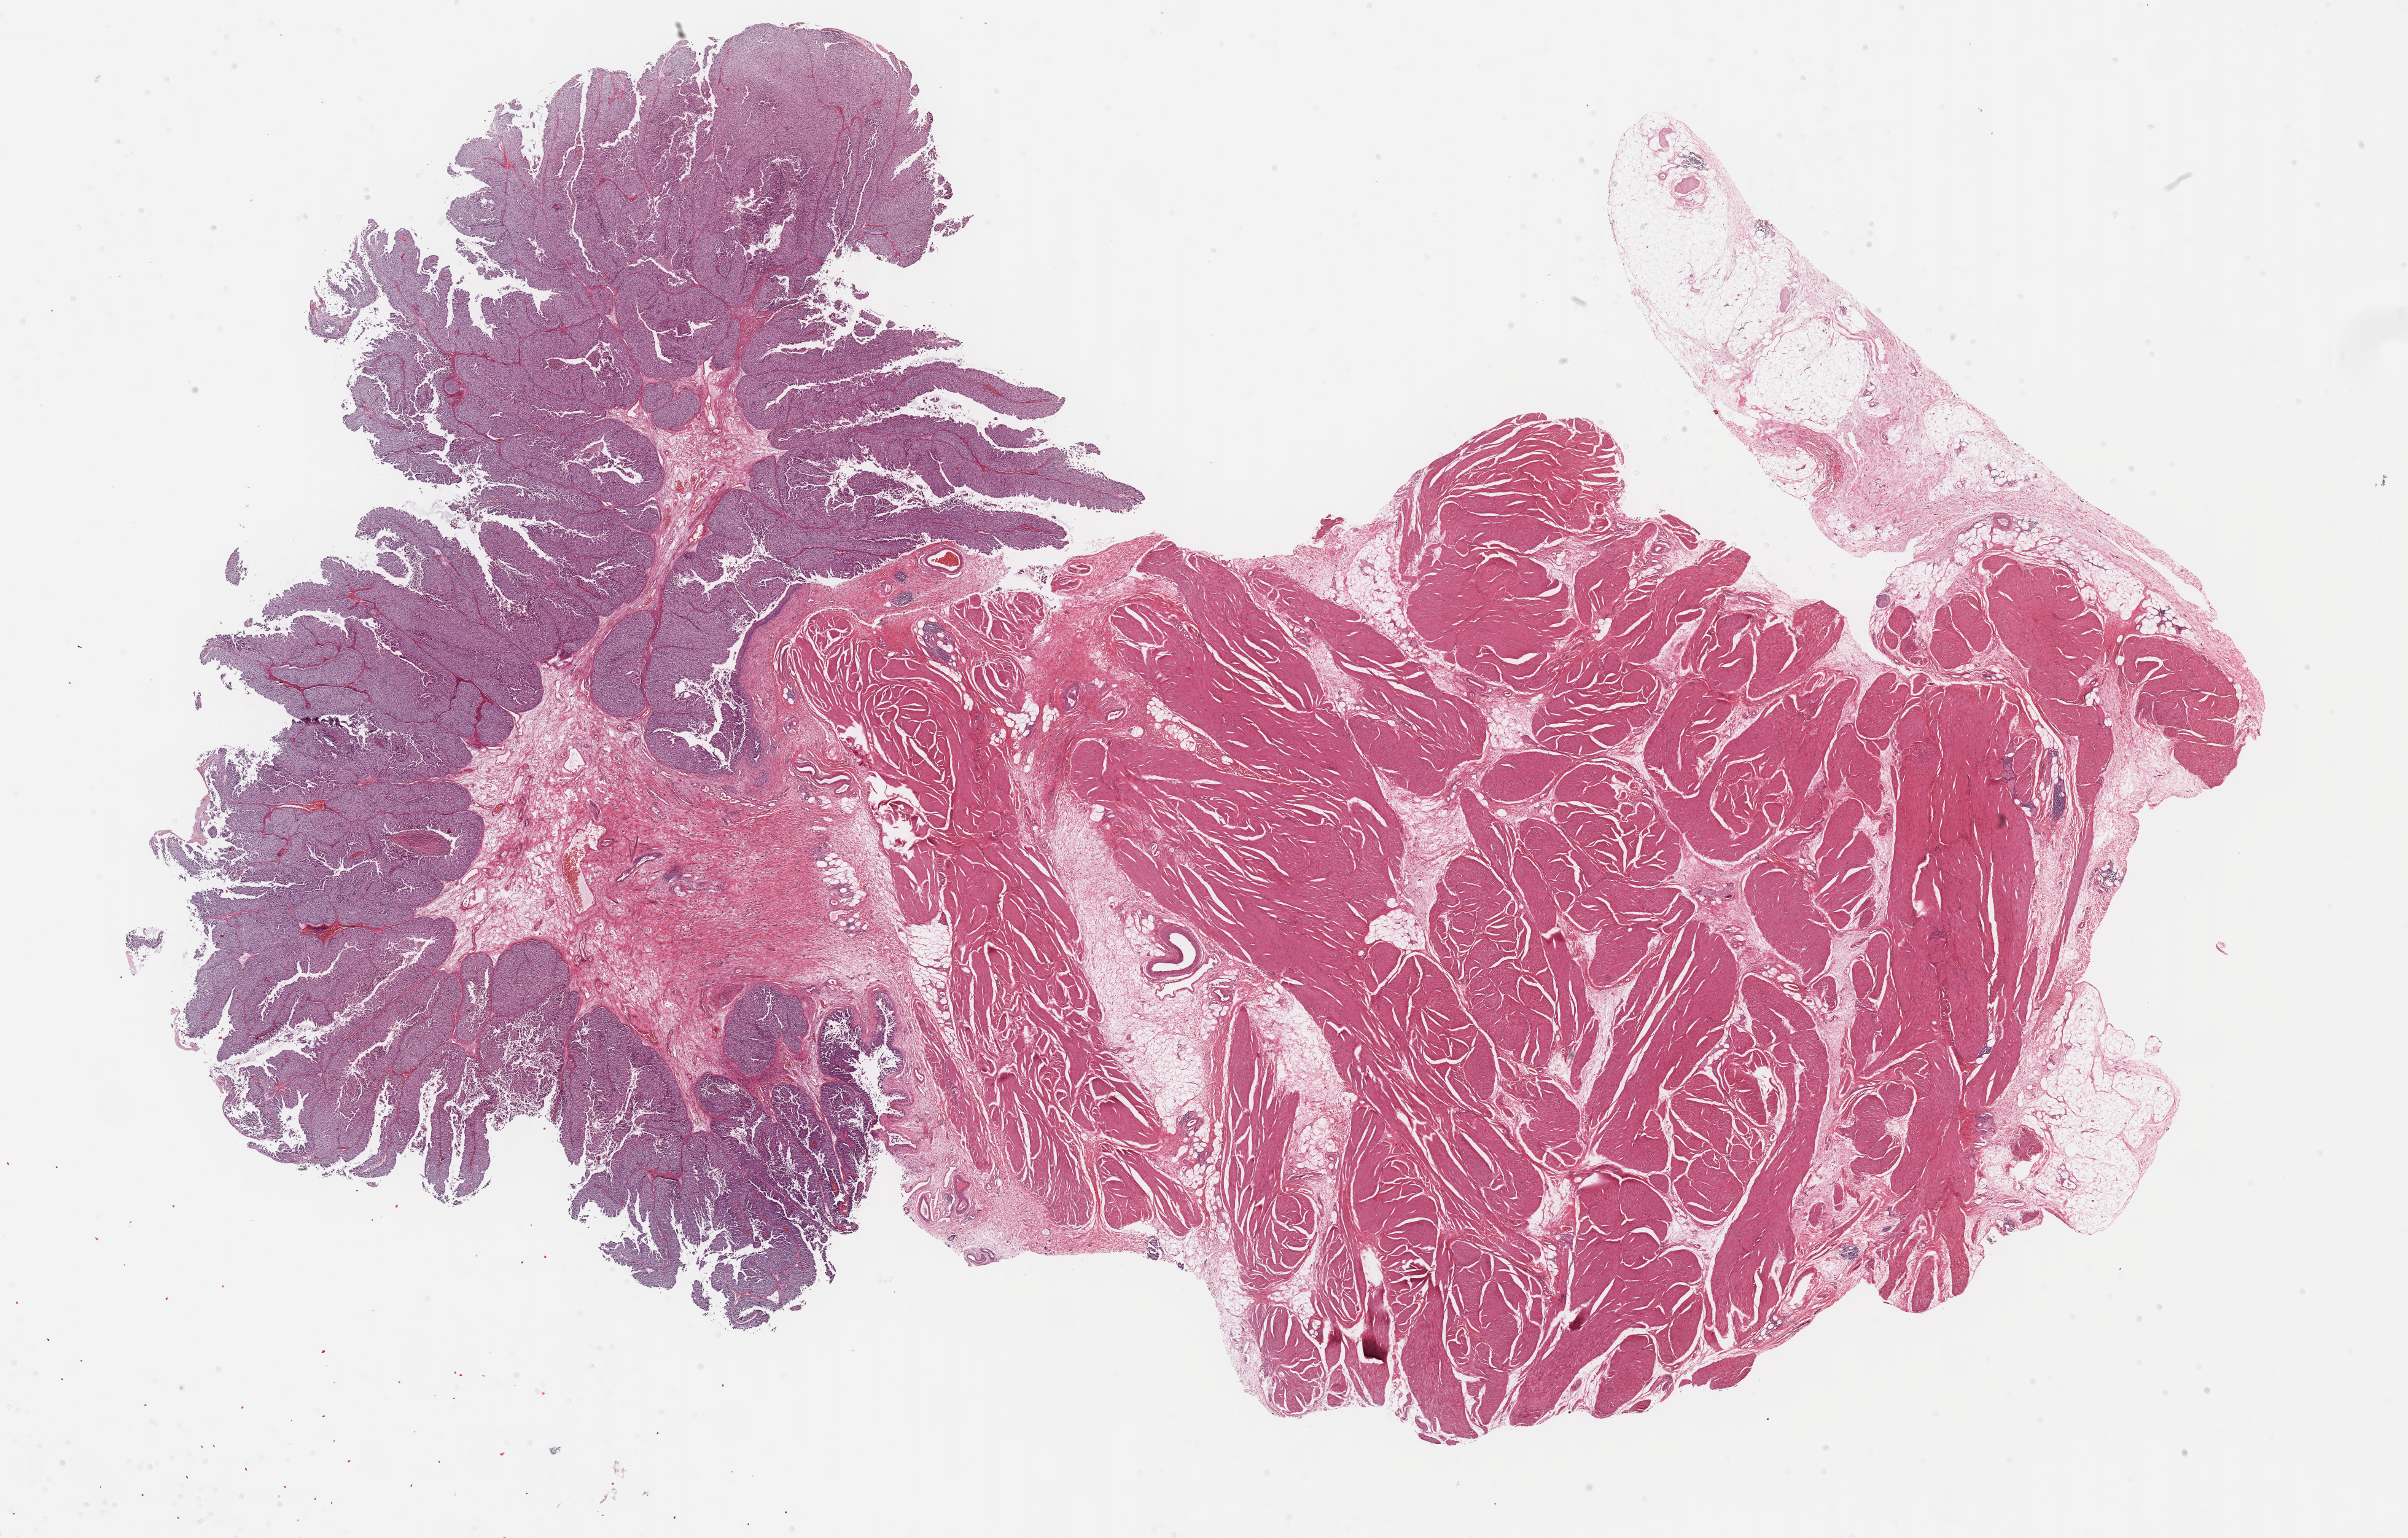
H&E-stained whole-slide image, low-resolution overview of the scanned area, about 31.7 x 20.3 mm (acquisition: 40x scan). FFPE section. Primary tumour sample from the bladder. Patient: male, age at initial diagnosis 79 years. Histologic grade: high grade.
- AJCC pathologic stage: IV
- TNM: T3a N2 MX
- diagnosis: Papillary transitional cell carcinoma
- lymph nodes positive (case pathology): 97 of 140 examined